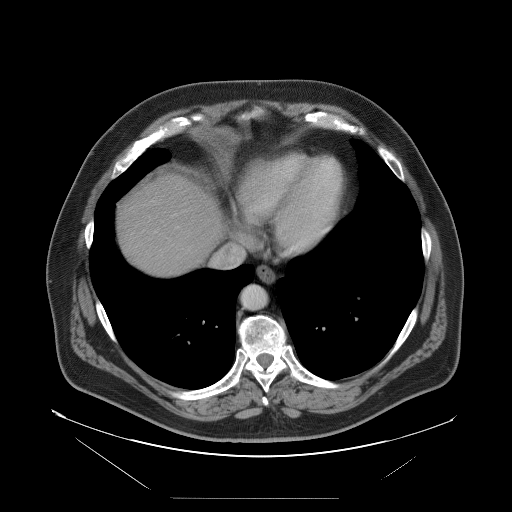
Contrast-enhanced abdominal CT, one axial slice. Slice 93 of 114 in the series (ordered by position). 120 kVp. Intravenous contrast given. Soft-tissue window (W 400 / L 40 HU). 5 mm slice thickness. 512 × 512 image matrix, field of view 500 × 500 mm. Male patient, age 61 years. Case-level facts recorded for this patient, not image findings: diagnosis: colorectal cancer liver metastases, imaged before liver resection; multiple liver metastases: no; largest metastasis: 6.5 cm; chemotherapy before resection: no.
Outlined on this slice (outlined manually by an expert reader):
- hepatic veins: bounding box [x1, y1, x2, y2] px = [213, 246, 244, 268]
- liver: [116, 175, 224, 275]
- planned liver remnant (the part of the liver to remain after resection): [164, 175, 225, 247]